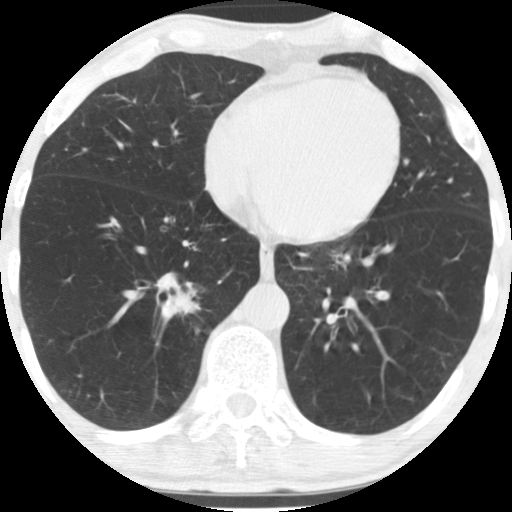
Low-dose screening chest CT, one axial slice; position 55 of 170 along the scan axis; 120 kVp; lung window (W 1500 / L -600 HU); 2.5 mm slice thickness; 512 × 512 image matrix, field of view 290 × 290 mm.
Structures marked on this image (outlined manually by an expert reader):
- lesion 1 (tumor, lower lobe of right lung): box from (x=172, y=290) to (x=197, y=313) px